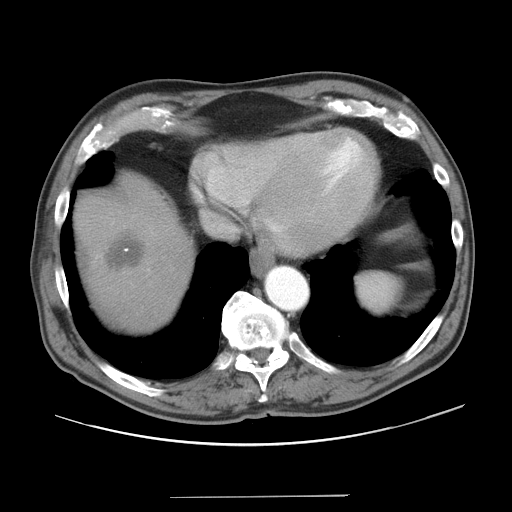
Contrast-enhanced abdominal CT, one axial slice; 120 kVp; intravenous contrast given; soft-tissue window (W 400 / L 40 HU); 512 × 512 image matrix. Male patient, age 75 years. From the clinical record (not read from this slice): diagnosis: colorectal cancer liver metastases, imaged before liver resection; multiple liver metastases: no; largest metastasis: 5.2 cm; disease in both lobes: no.
Structures marked on this image (manually delineated by an expert):
- hepatic veins: box from (x=203, y=212) to (x=236, y=232) px
- liver: (x=77, y=185)–(x=191, y=328)
- planned liver remnant (the part of the liver to remain after resection): (x=117, y=251)–(x=191, y=328)
- liver metastasis: (x=108, y=236)–(x=145, y=269)